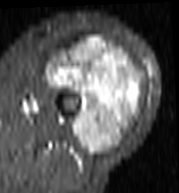
MRI of an extremity soft-tissue mass, one axial slice. Slice 55 of 103 in the series (ordered by position). STIR. MR volume resampled by the dataset authors to the PET/CT grid (not the native acquisition matrix). 3.27 mm slice thickness. 179 × 193 image matrix, field of view 175 × 188 mm. Female patient. Case-level facts recorded for this patient, not image findings: histological type: undifferentiated – high grade; grade: high; site of the primary tumour: left thigh.
Outlined on this slice (expert contour drawn on MRI and transferred to this co-registered scan by the dataset authors):
- gross tumour volume including surrounding oedema: bounding box [x1, y1, x2, y2] px = [47, 37, 144, 156]
- gross tumour volume (mass): [47, 37, 142, 156]